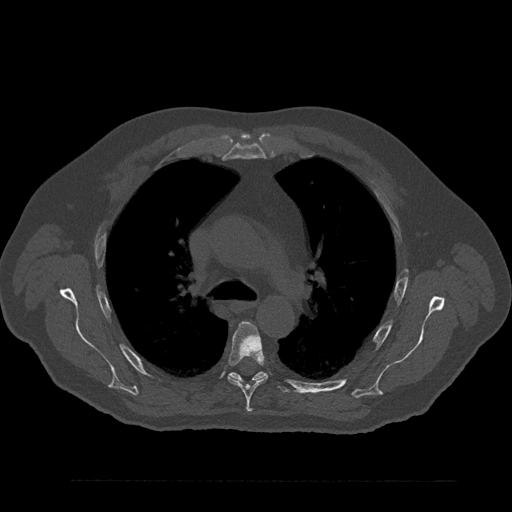
CT including the spine, one axial slice; slice 592 of 797 in the series (ordered by position); reconstruction kernel Br40s/3; 120 kVp; bone window (W 1800 / L 400 HU); 0.5 mm slice thickness; 512 × 512 image matrix. Male patient, age 61 years. Case-level facts recorded for this patient, not image findings: primary cancer: prostate.
Outlined on this slice (semi-automatic segmentation, software-assisted and operator-edited):
- T5 vertebra: bounding box [x1, y1, x2, y2] px = [228, 322, 268, 413]
- T6 vertebra: [228, 364, 290, 393]